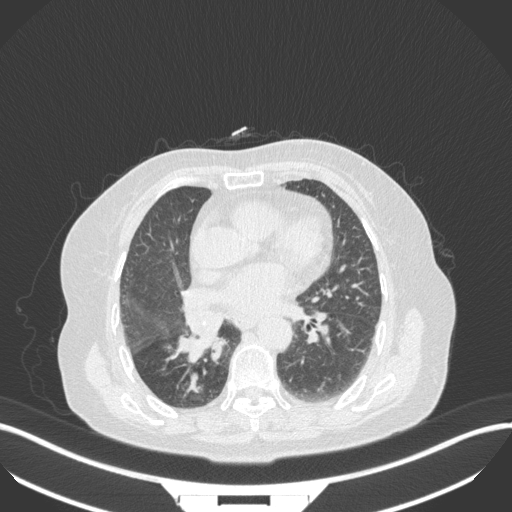
Chest CT, one axial slice; slice 148 of 329 in the series (ordered by position); reconstruction kernel B31f; 120 kVp; lung window (W 1500 / L -600 HU); 512 × 512 image matrix, field of view 400 × 400 mm. Patient: female, 75 years. From the clinical record (not read from this slice): clinical TNM (as recorded): T1b N0 M1a; histopathological grade: G1.
Annotated regions visible in this slice (bounding box drawn by a radiologist):
- lung tumour (recorded histology: squamous cell carcinoma): bounding box [x1, y1, x2, y2] px = [175, 315, 225, 364]